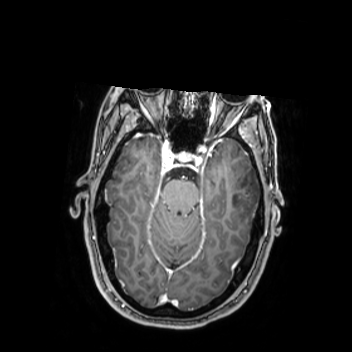
Brain MRI from a brain-tumour surgery series, one axial slice. Slice 168 of 350 in the series (ordered by position). T1-weighted post-contrast. 352 × 352 image matrix, field of view 280 × 280 mm. Case-level facts recorded for this patient, not image findings: histopathology: Oligodendroglioma; WHO grade: 2; IDH mutation: yes.
Structures marked on this image (manually delineated by an expert):
- tumour: box from (x=224, y=163) to (x=262, y=222) px